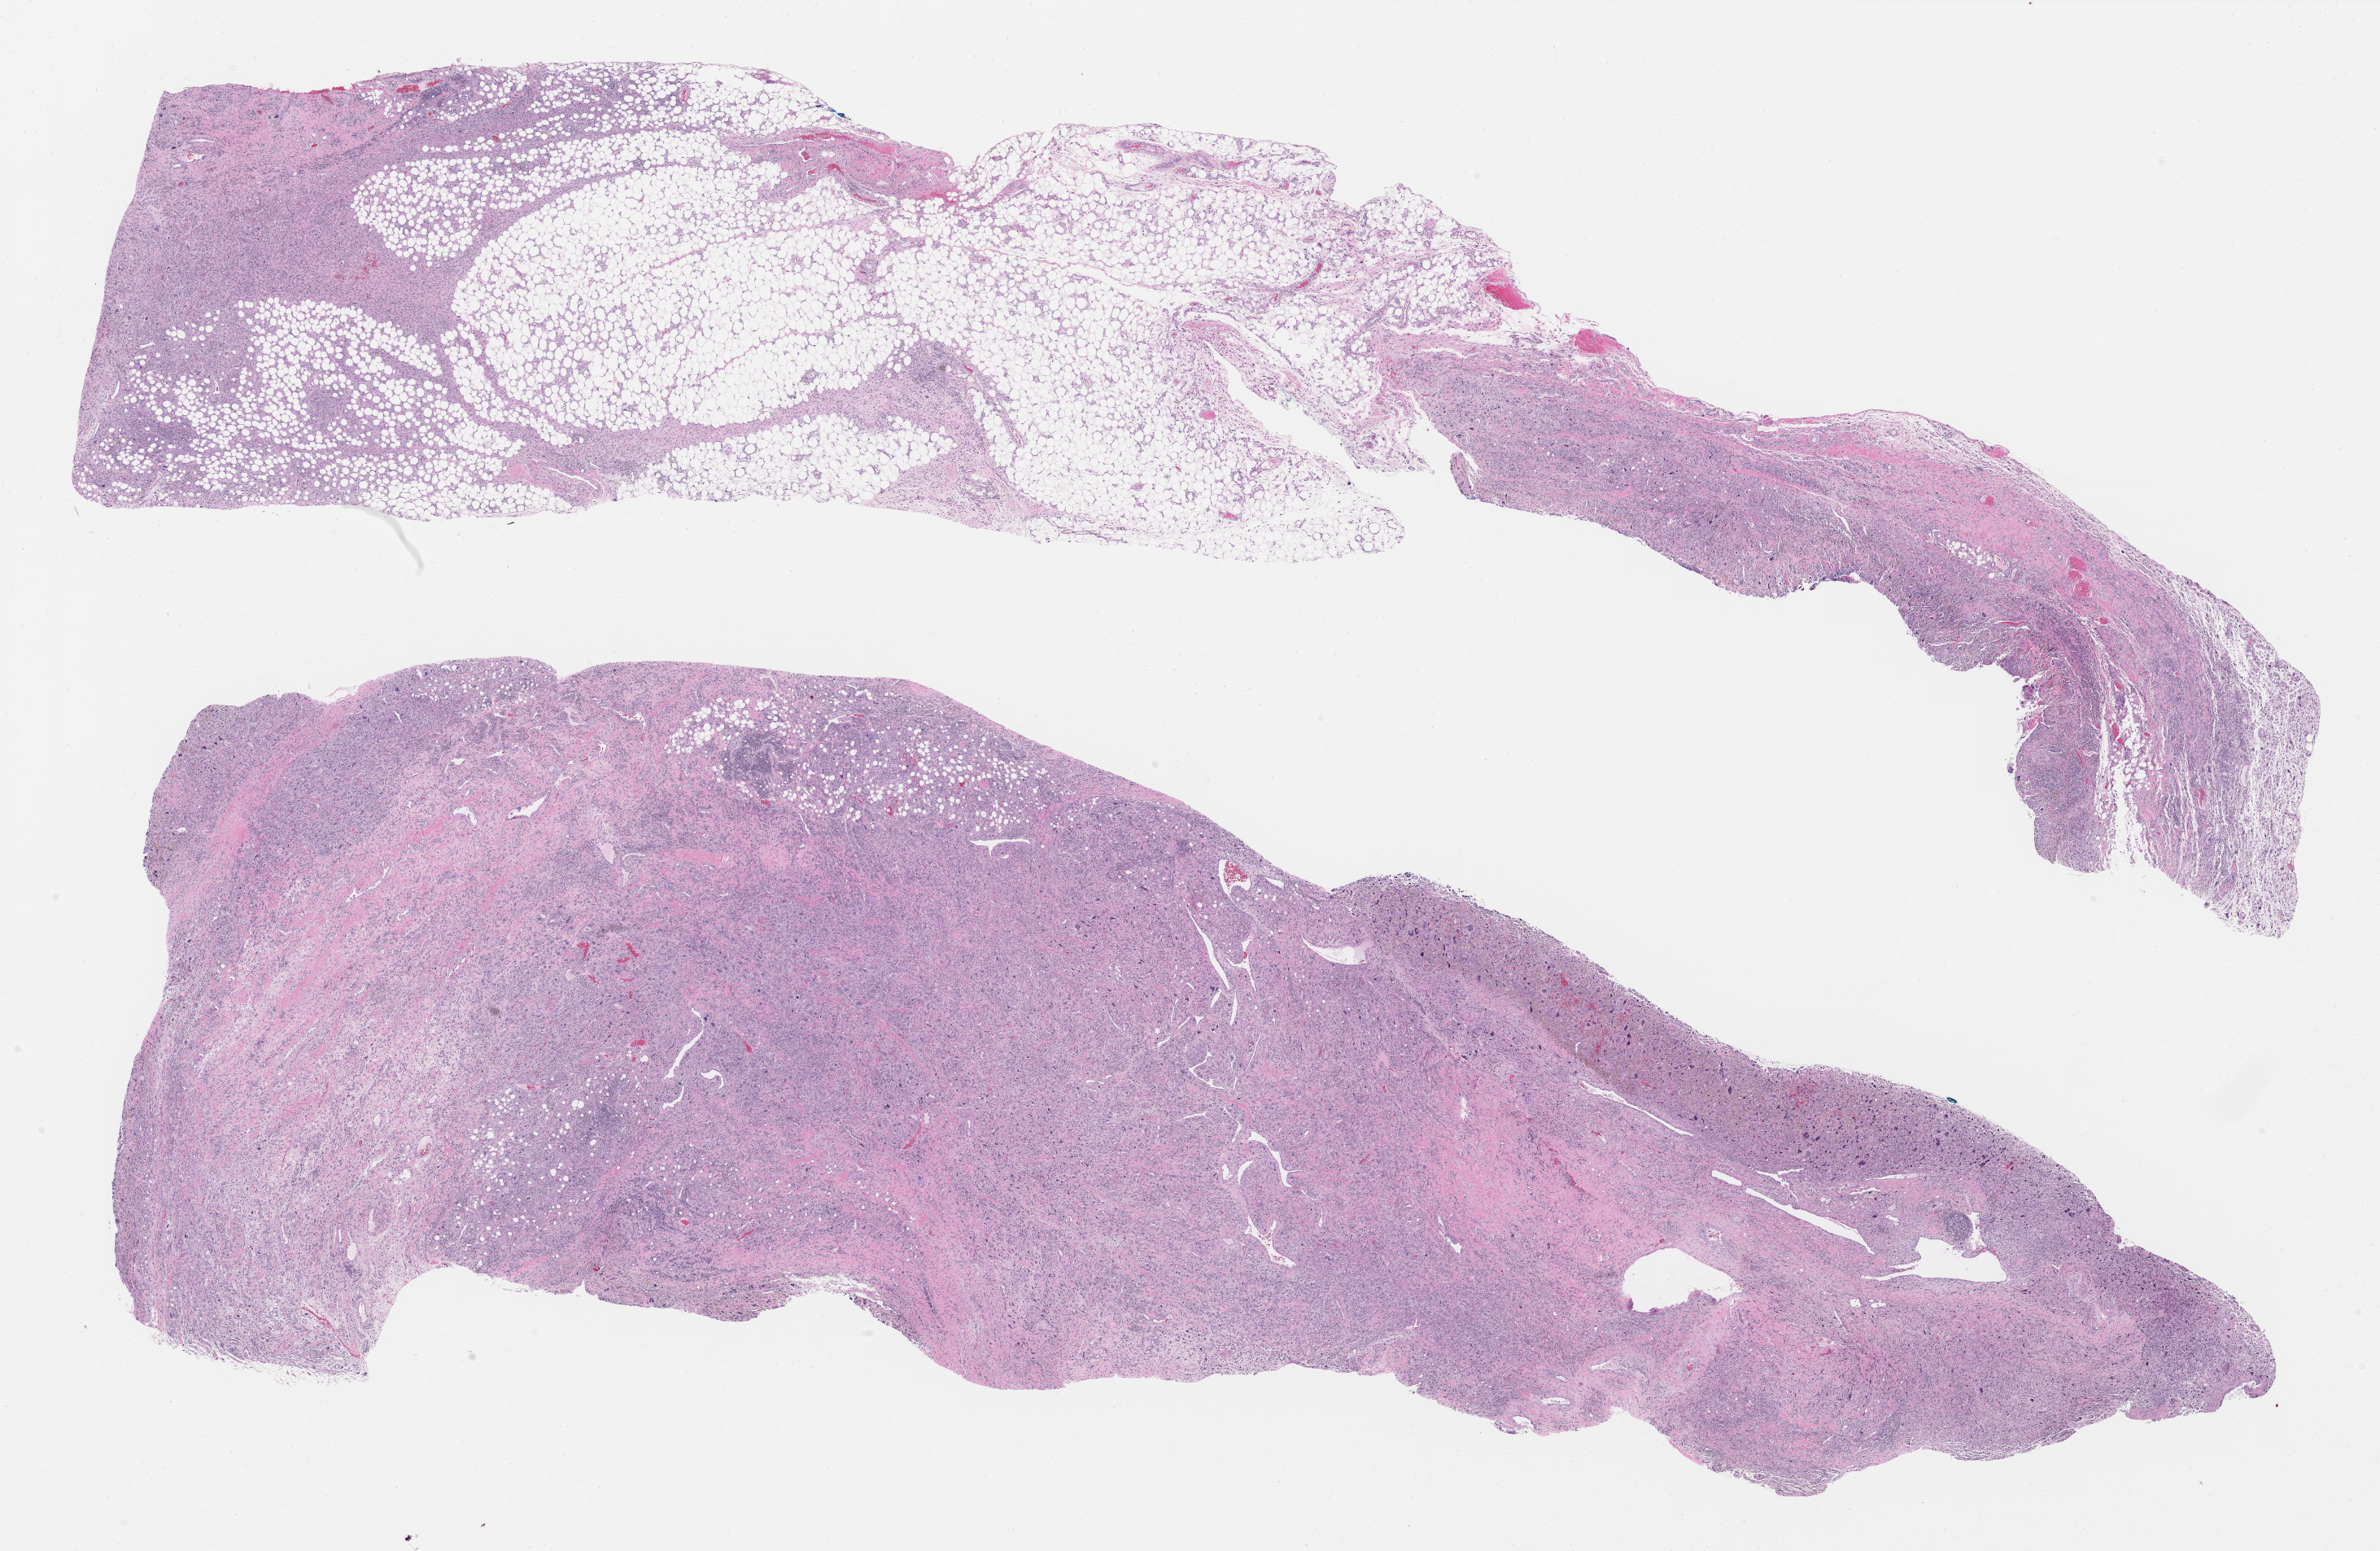
Whole-slide histology image, H&E, low-resolution overview of the scanned area, about 23.5 x 15.3 mm (from a 40x scan), formalin-fixed paraffin-embedded (FFPE) diagnostic section, connective, subcutaneous and other soft tissues, primary tumour sample. Patient: male, age at initial diagnosis 71 years.
- pathologic diagnosis: Undifferentiated sarcoma (connective, subcutaneous and other soft tissues of trunk, NOS)